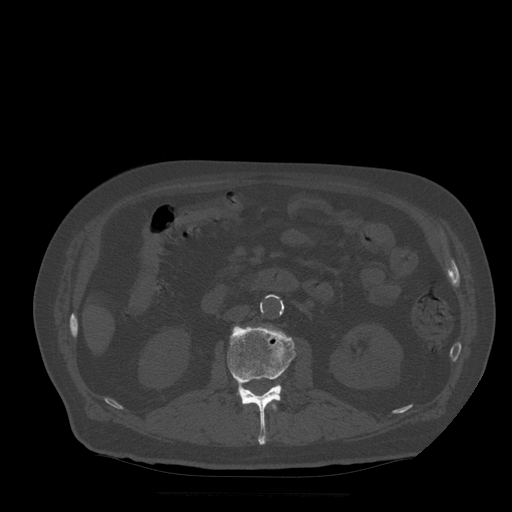
CT including the spine, one axial slice; slice 166 of 522 in the series (ordered by position); bone window (W 1800 / L 400 HU); 1.25 mm slice thickness; 512 × 512 image matrix. Patient age 72 years. From the clinical record (not read from this slice): primary cancer: prostate.
Outlined on this slice (semi-automatic segmentation, software-assisted and operator-edited):
- L1 vertebra: bounding box <272,404,277,411> (left, top, right, bottom; pixels)
- L2 vertebra: <228,326,296,445>